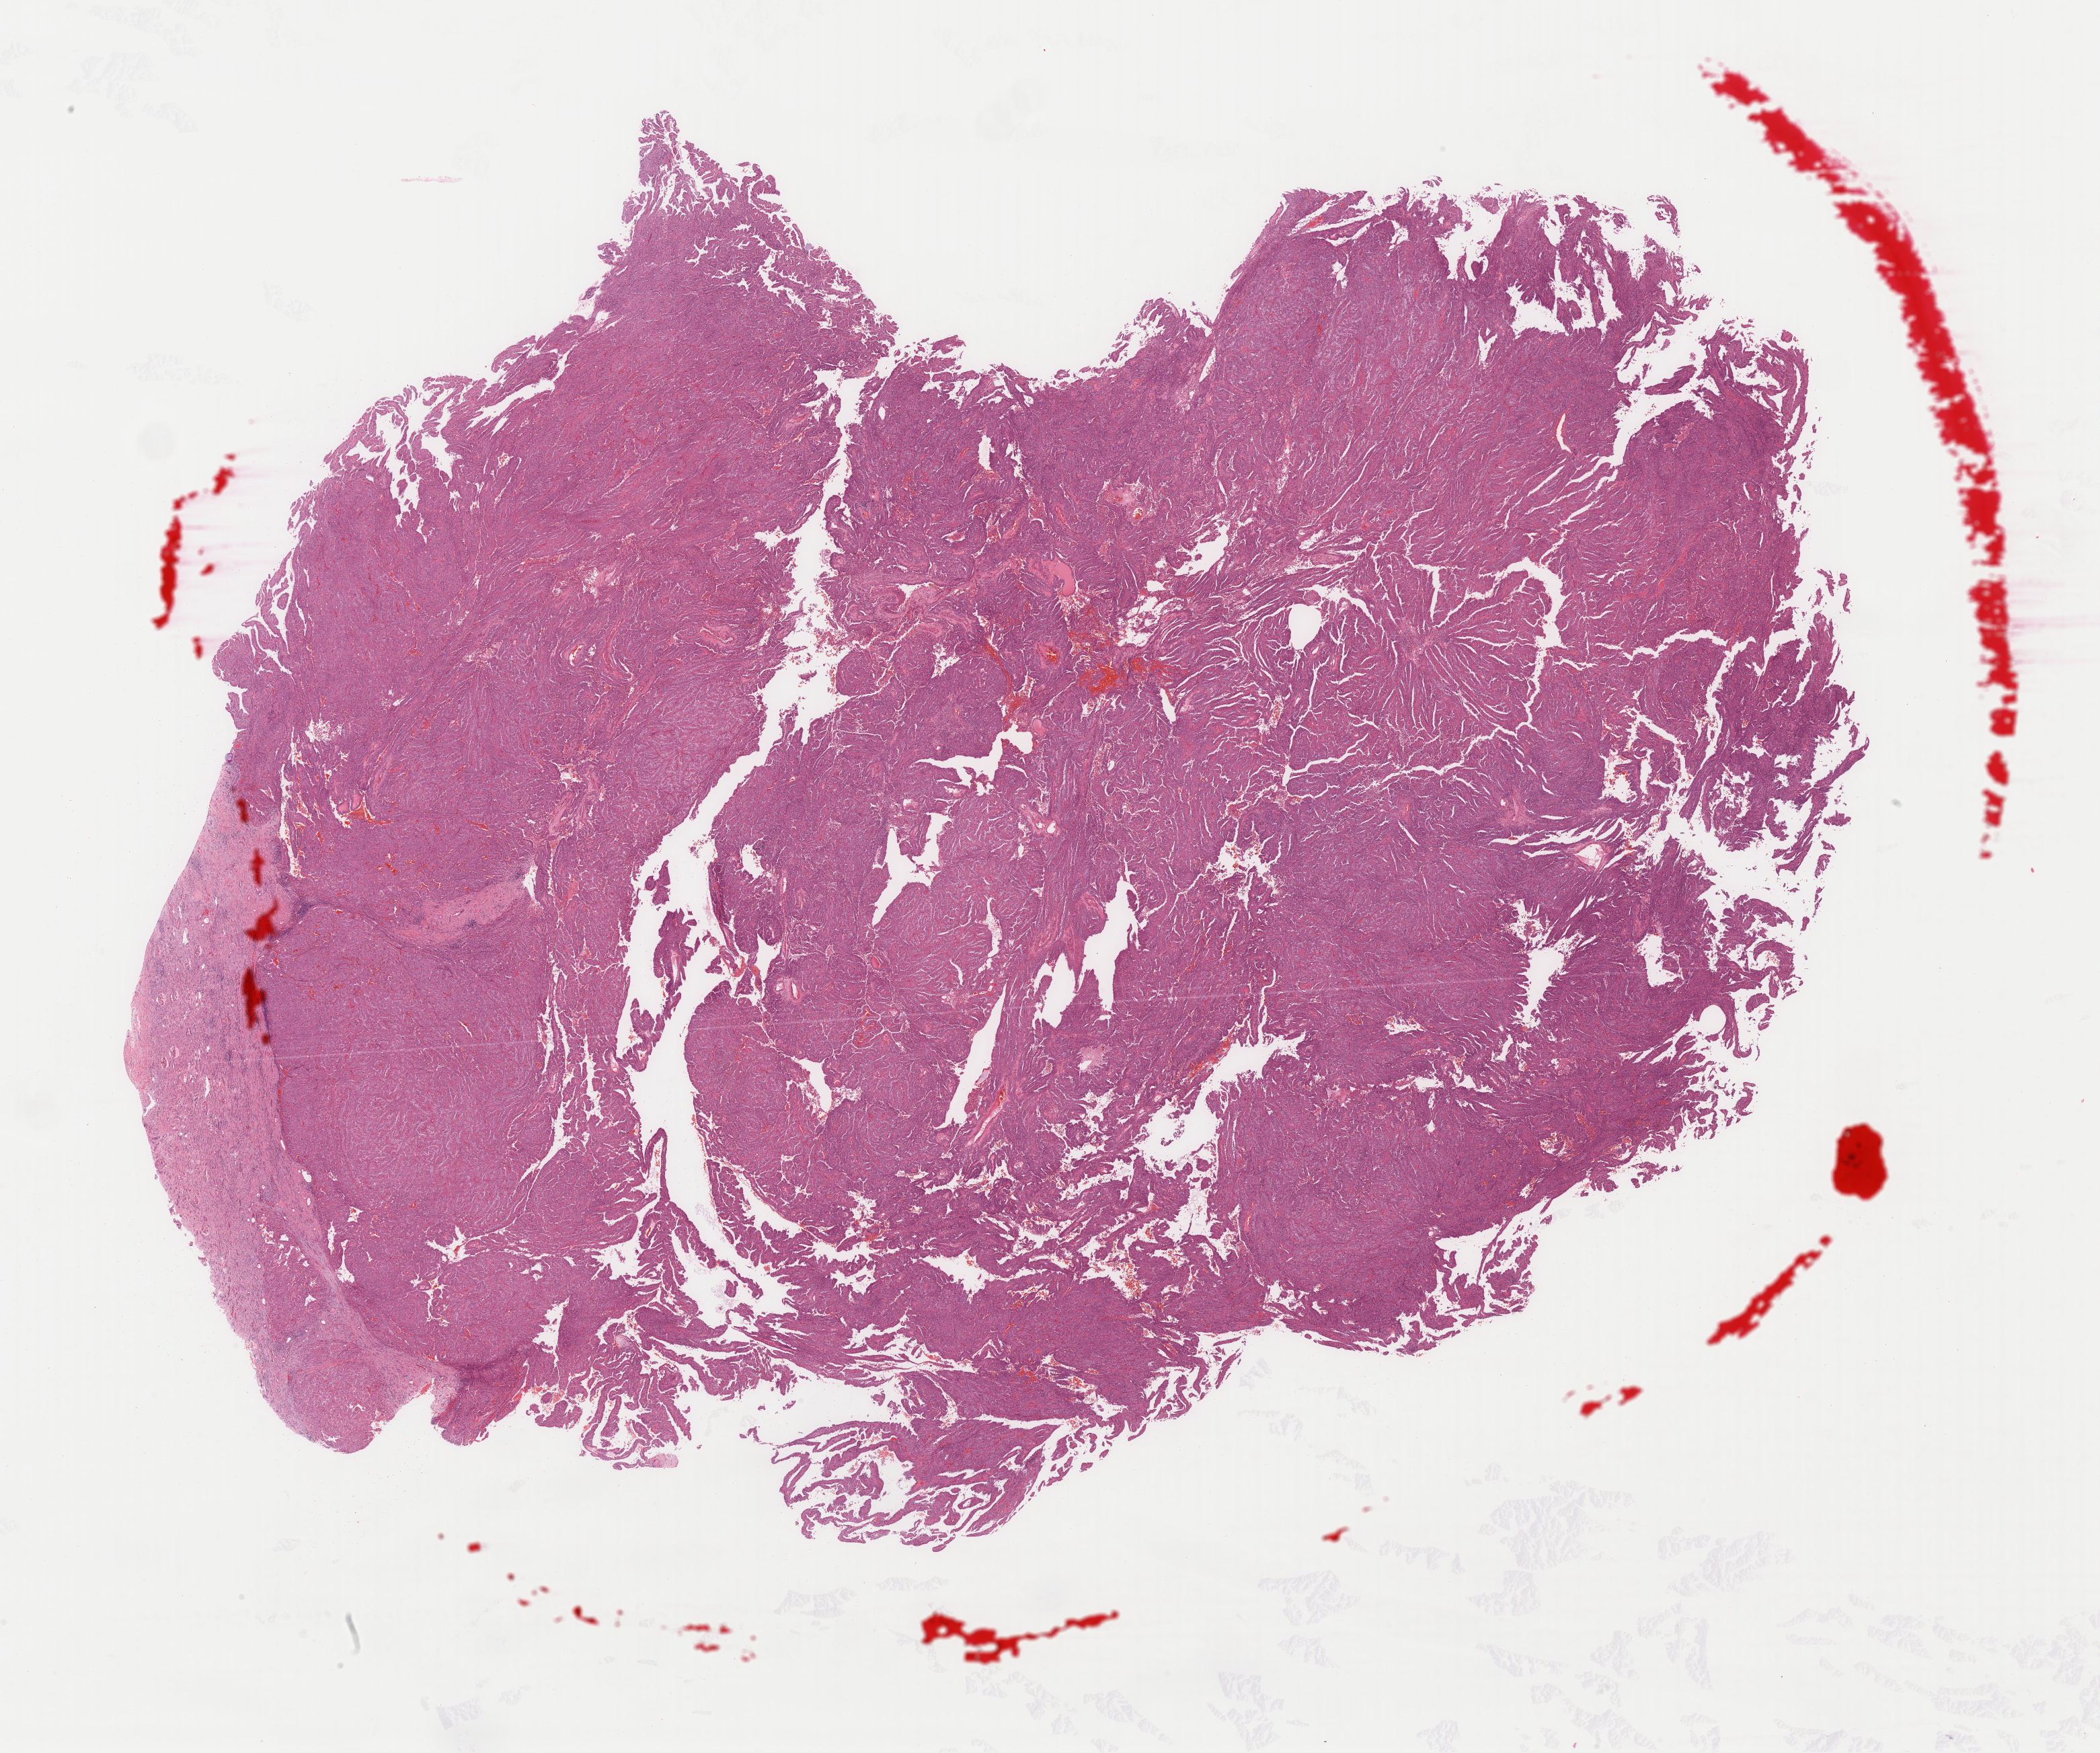
H&E-stained whole-slide image, shown as a low-resolution overview of the whole scanned area (about 24.7 x 20.6 mm). Formalin-fixed paraffin-embedded (FFPE) diagnostic section. Primary tumour sample from the kidney. Female, age 35 years at initial diagnosis.
• TNM: T3a NX MX
• AJCC pathologic stage: III
• laterality: left
• pathologic diagnosis: Papillary adenocarcinoma, NOS